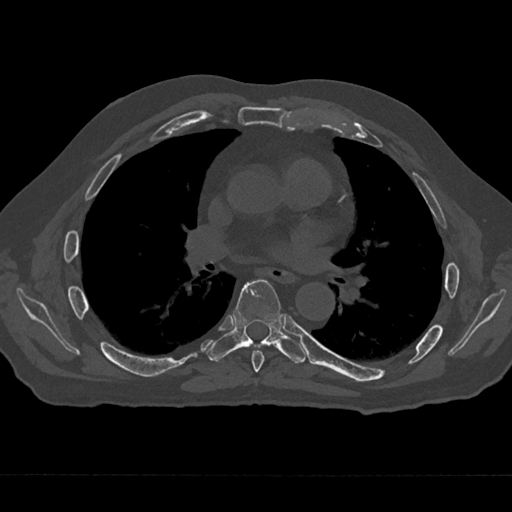
CT including the spine, one axial slice. Slice 389 of 797 in the series (ordered by position). 120 kVp. Bone window (W 1800 / L 400 HU). 0.5 mm slice thickness. 512 × 512 image matrix, field of view 377 × 377 mm. Male patient, age 75 years. Case-level facts recorded for this patient, not image findings: primary cancer: renal; vertebrae with lytic lesions (as recorded): T4.
Structures marked on this image (semi-automatic segmentation, software-assisted and operator-edited):
- T6 vertebra: bounding box [x1, y1, x2, y2] px = [252, 350, 265, 372]
- T7 vertebra: [207, 279, 306, 363]